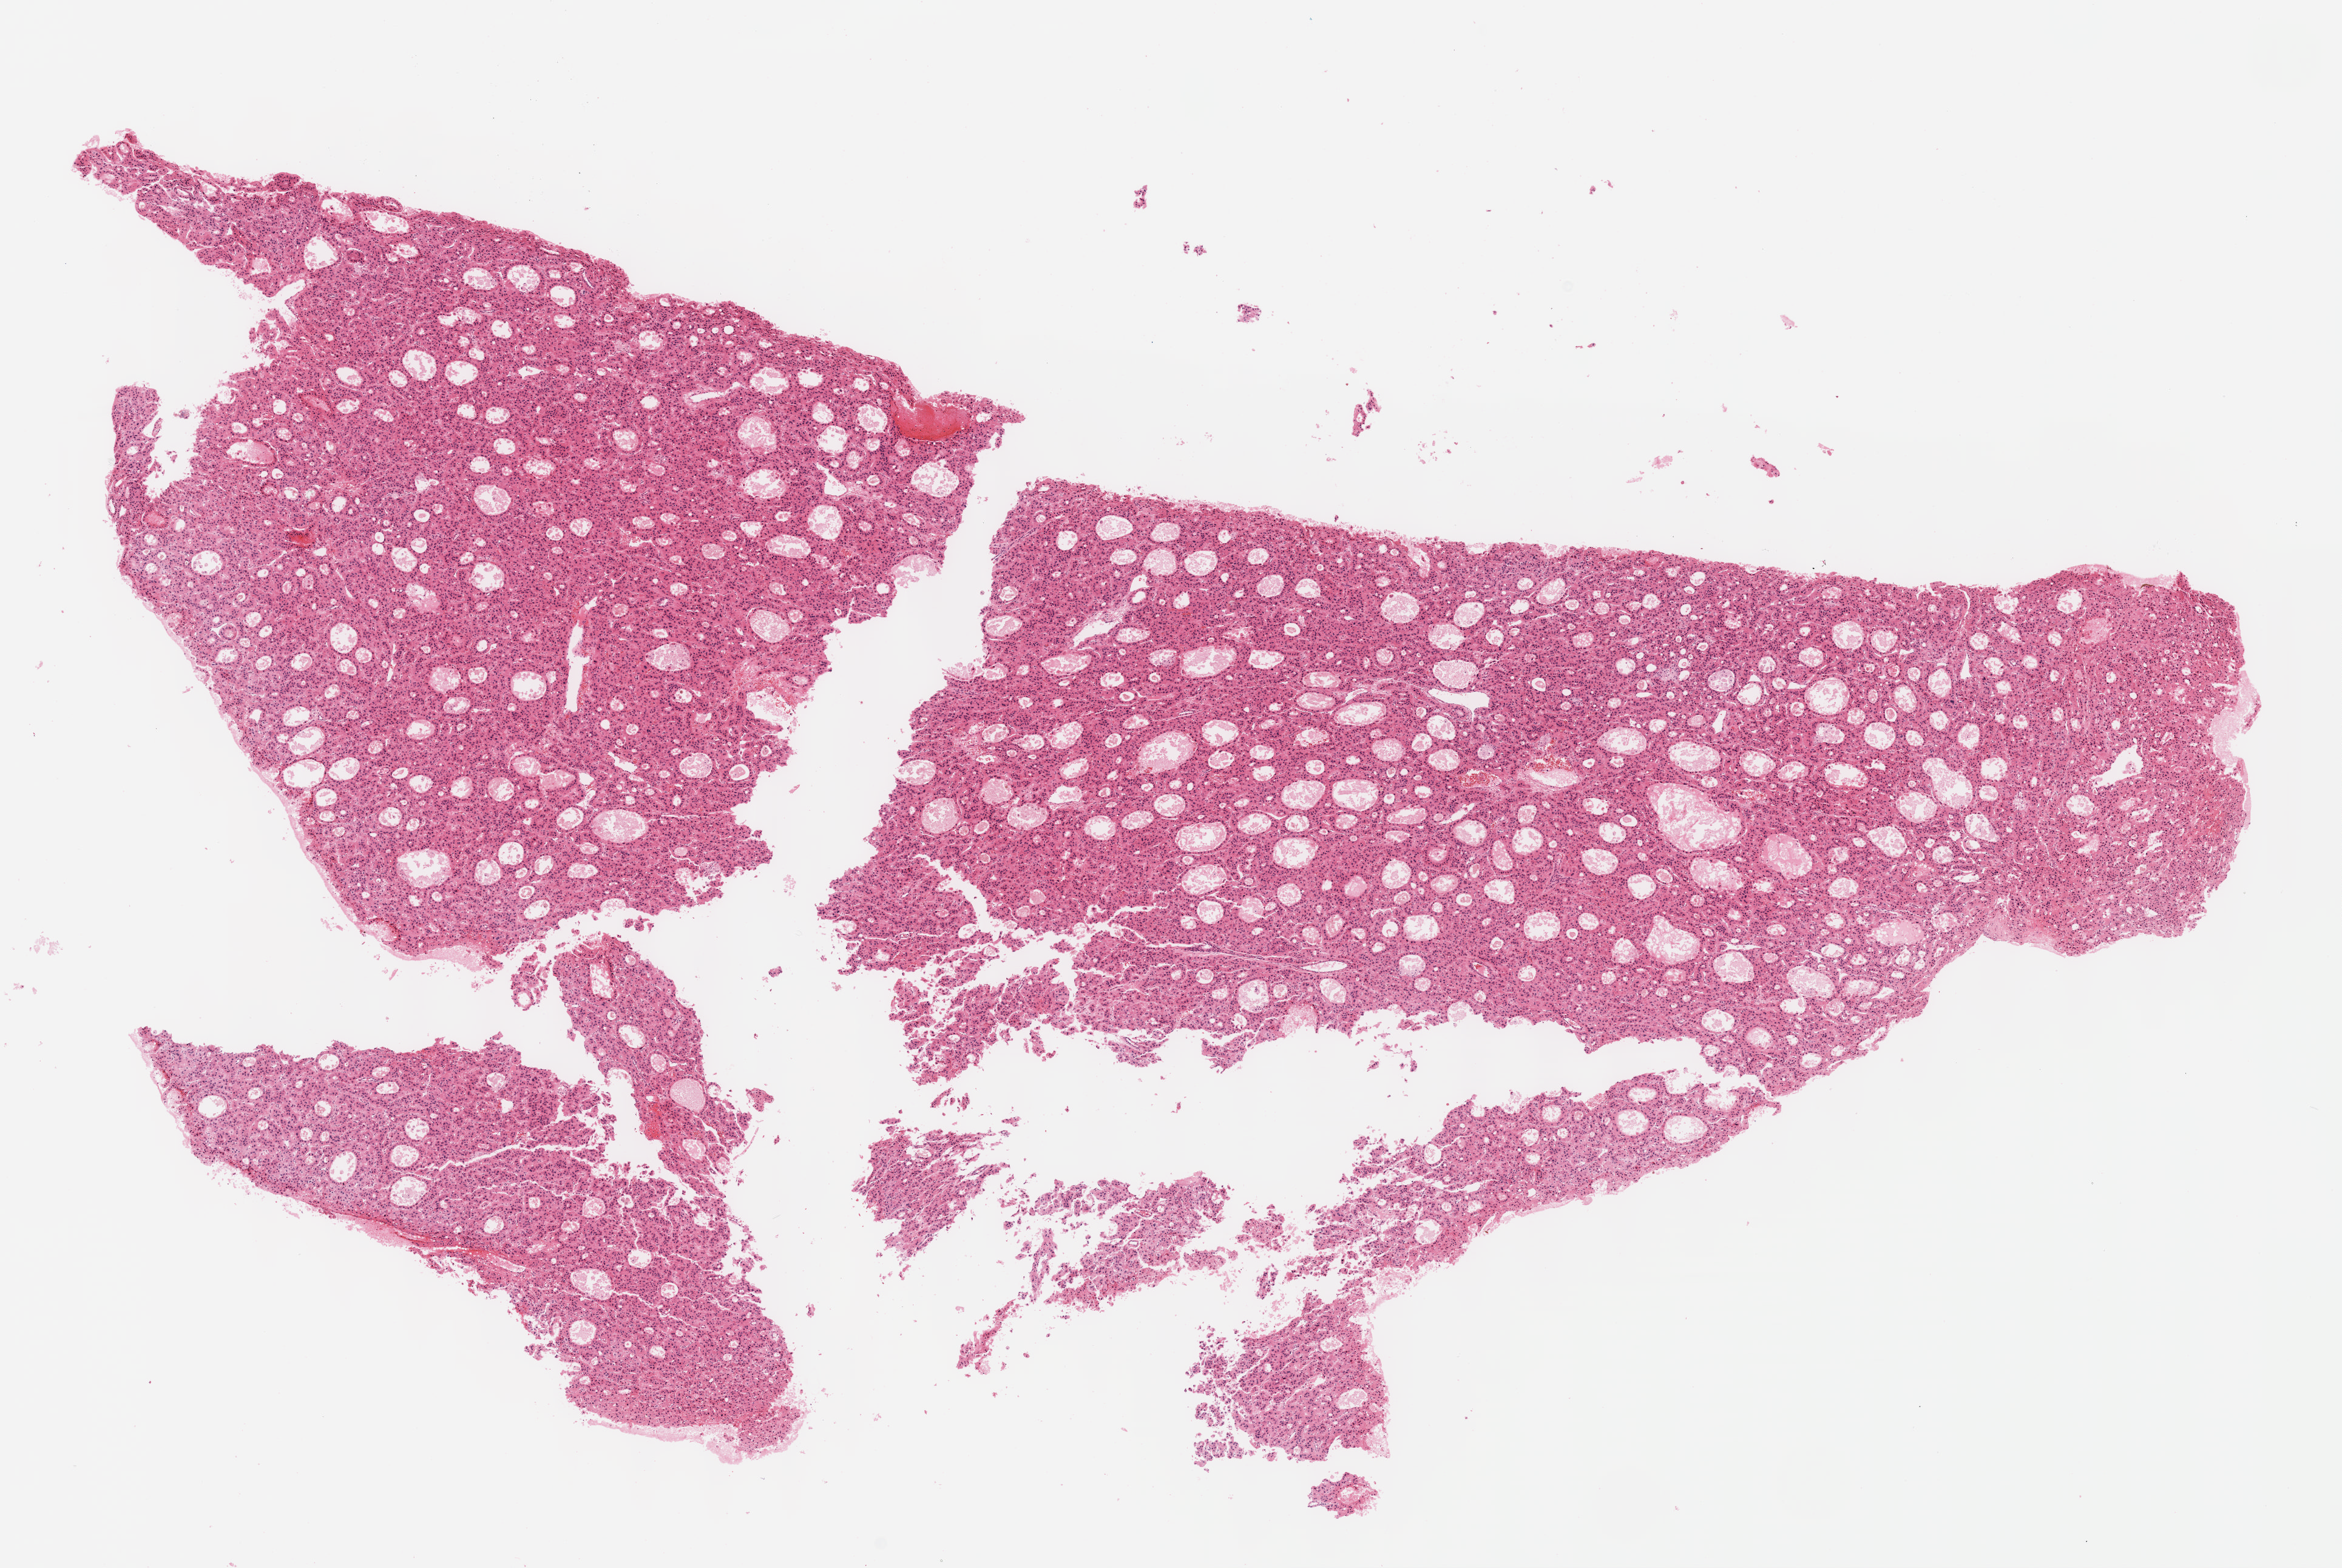
Digitized H&E-stained tissue section (whole slide), whole scanned area (about 15.6 x 10.4 mm) shown as a low-resolution overview; formalin-fixed paraffin-embedded (FFPE) diagnostic section; primary tumour sample from the liver. Male, age 50 years at initial diagnosis. Histologic grade: G2 (moderately differentiated).
- histologic diagnosis: Hepatocellular carcinoma, NOS
- TNM: T1 N0 M0
- AJCC pathologic stage: I (7th edition)